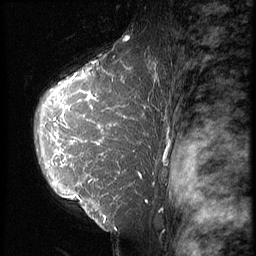
Breast MRI (dynamic contrast-enhanced), one sagittal slice. 3 images stored at this slice position (order not interpretable as contrast timing). 1.5 T. TE 4.2 ms, TR 9 ms. 256 × 256 image matrix. Patient: female, 39 years. Case-level facts recorded for this patient, not image findings: setting: breast cancer imaged before/during neoadjuvant chemotherapy; receptor status: HER2-positive.
Annotated regions visible in this slice (semi-automatically segmented with operator editing):
- analysis volume of interest (the breast-tissue region the enhancement analysis was run in; not a lesion): box from (x=31, y=47) to (x=151, y=239) px
- tumour enhancement mask (voxels above the 140 % enhancement threshold inside the analysis volume of interest): (x=51, y=67)–(x=146, y=231)